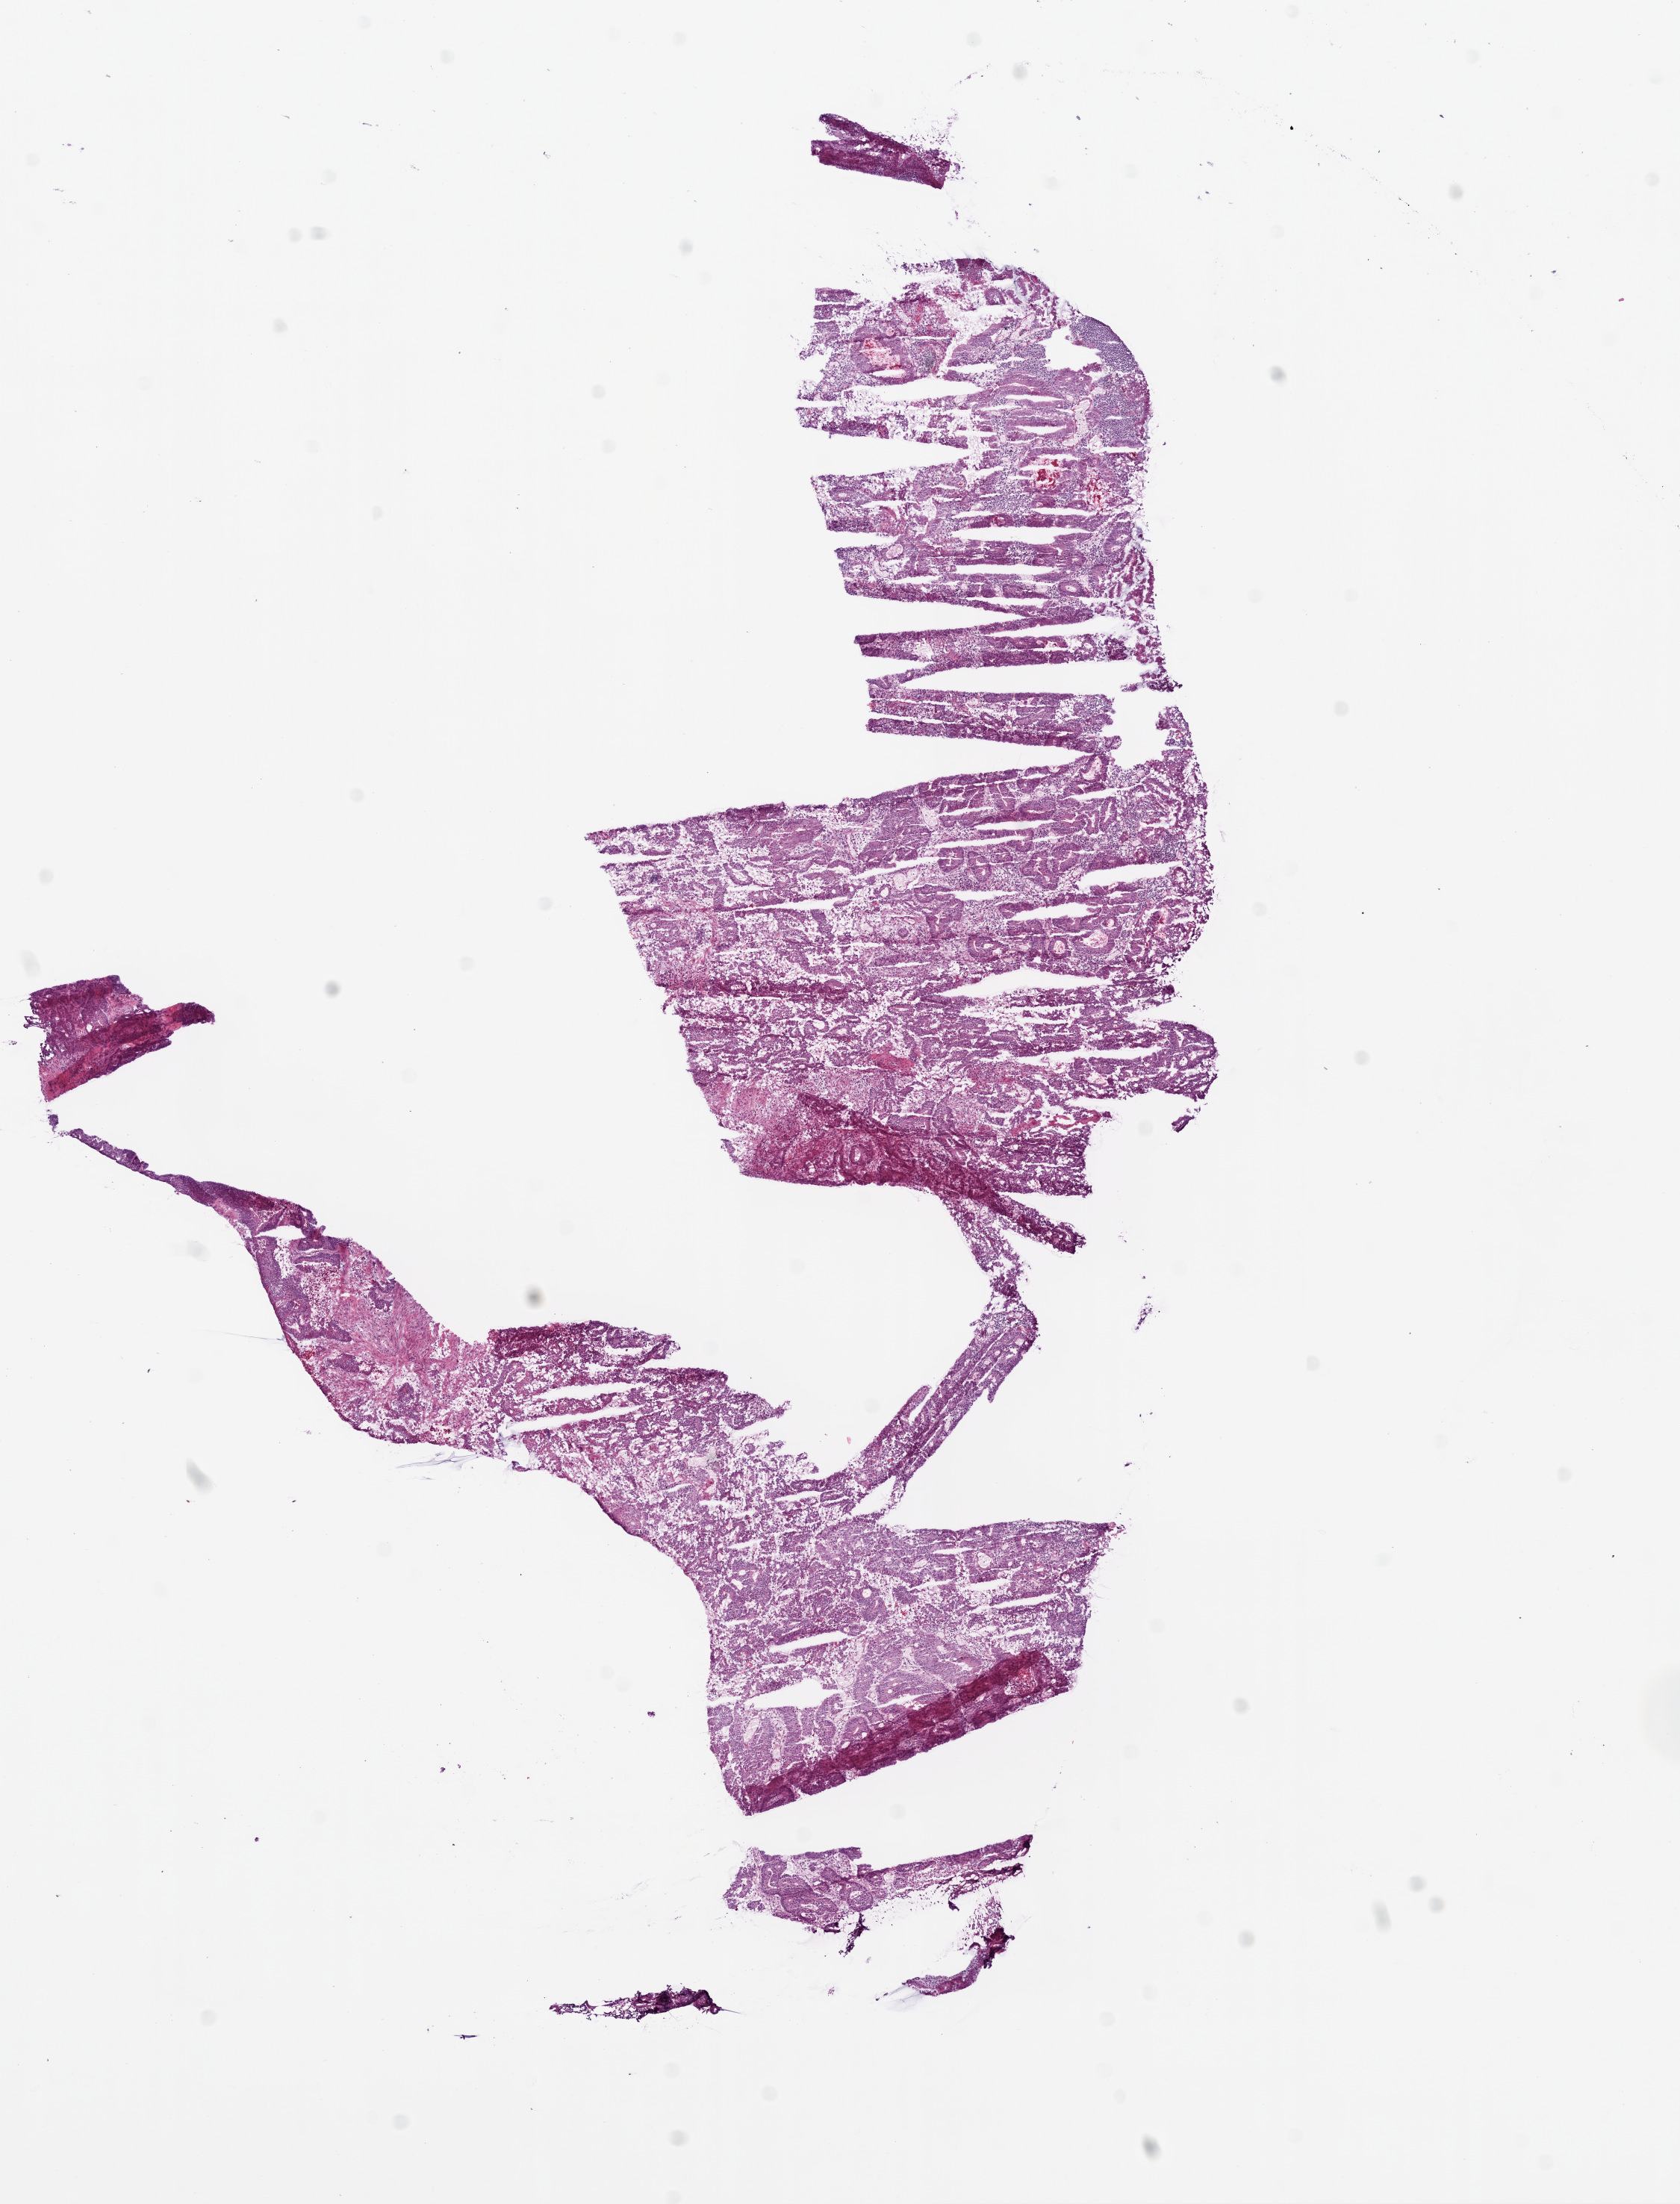
Hematoxylin and eosin (H&E) stained whole-slide image, low-resolution overview of the scanned area, about 9.0 x 11.8 mm (from a 20x scan); frozen section; sample: primary tumour, colon. Female patient; age at initial diagnosis 53 years. Slide review estimates, as recorded: tumour cells 85%, tumour nuclei 80%, normal cells 0%, stromal cells 10%, necrosis 5%.
• pathologic diagnosis: Adenocarcinoma, NOS (sigmoid colon)
• AJCC pathologic stage: IIIB (6th edition)
• lymph nodes positive (case pathology): 2 of 14 examined